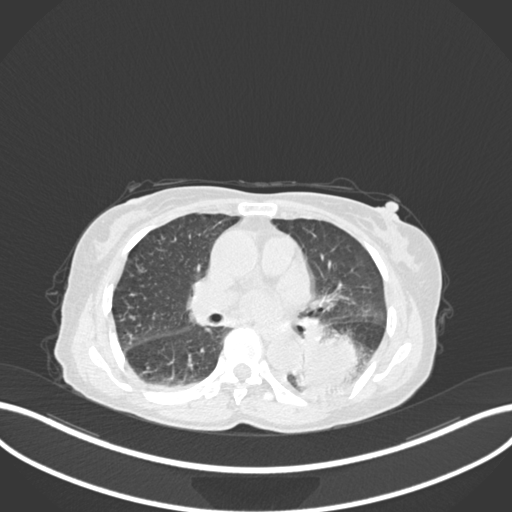
Chest CT, one axial slice. Position 90 of 233 along the scan axis. Reconstruction kernel B30f. 120 kVp. Lung window (W 1500 / L -600 HU). 1 mm slice thickness. 512 × 512 image matrix. Patient: female, 78 years. Case-level facts recorded for this patient, not image findings: clinical TNM (as recorded): T3 N0 M1.
Annotated regions visible in this slice (rectangle marked by the reading radiologist):
- lung tumour (recorded histology: squamous cell carcinoma): bounding box (x1, y1, x2, y2) in pixels: (298, 330, 366, 400)